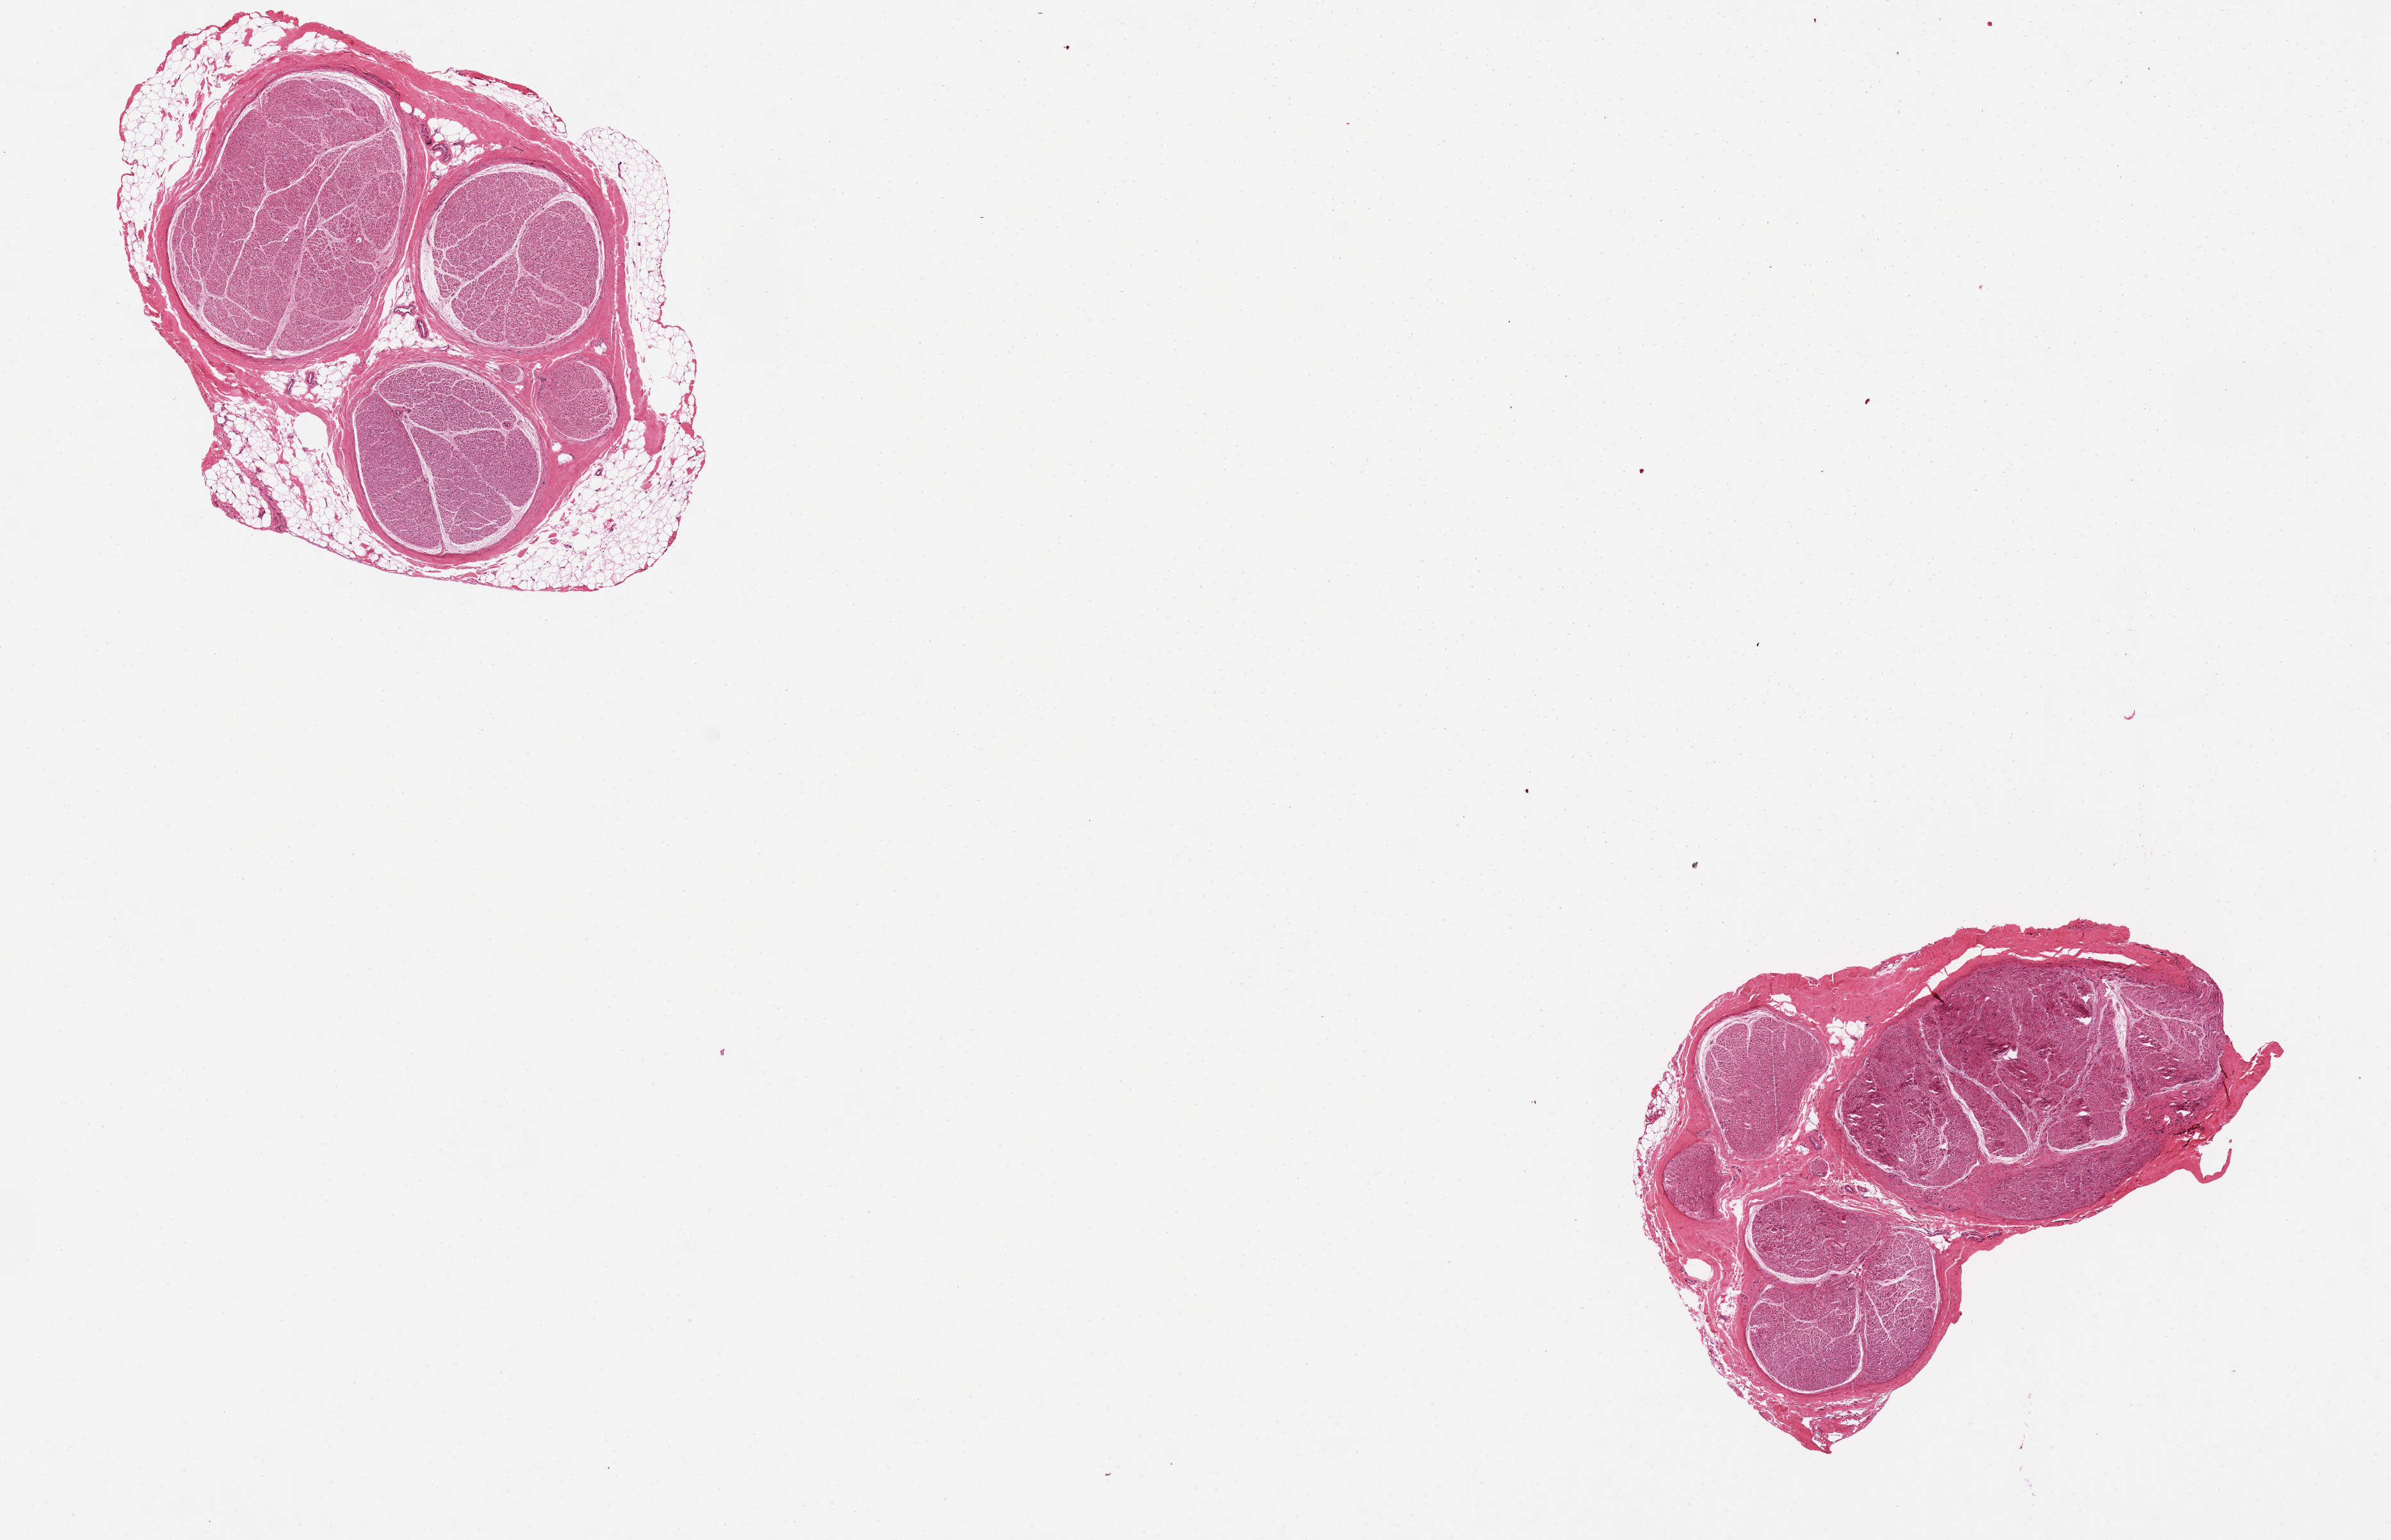
Digitized H&E-stained section, shown as a low-resolution overview of the whole scanned area (about 14.8 x 9.5 mm), PAXgene-fixed paraffin-embedded (PFPE) section, sampled site (target tissue): tibial nerve, donor tissue sample. Male donor.
Pathologist's review note for this sample: Two sections, 4x3mm; one with 20% fat.